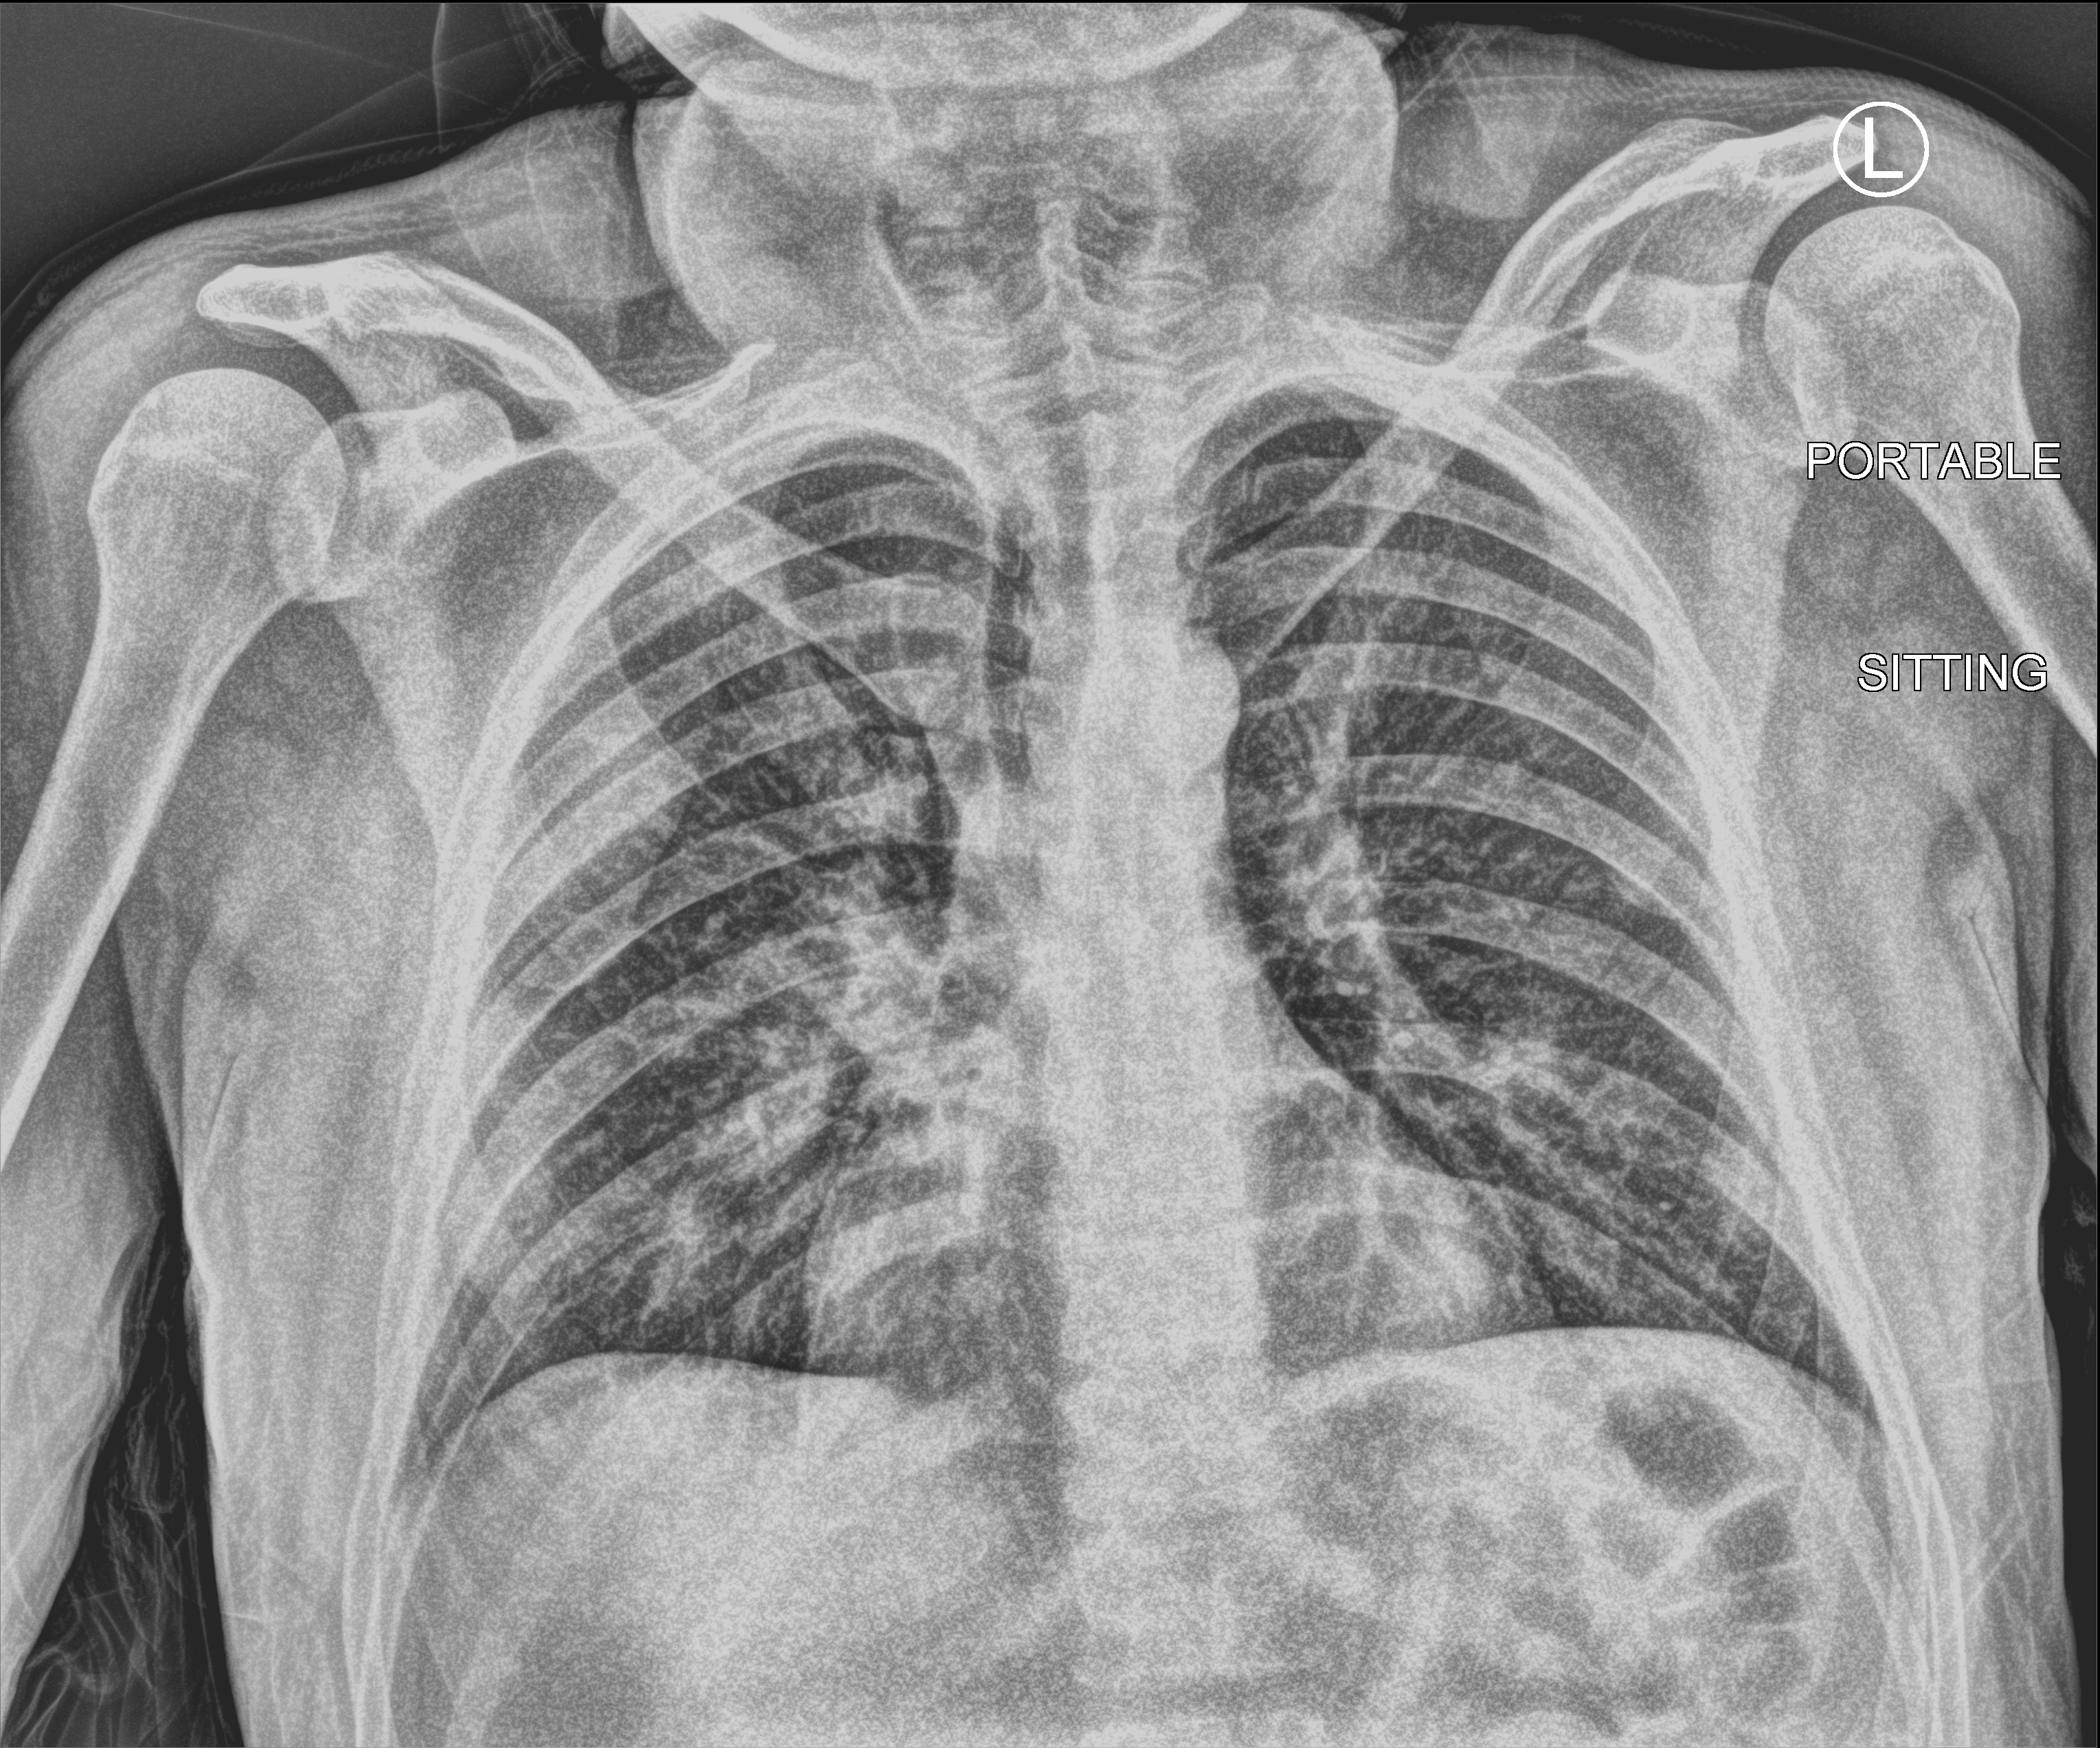
Portable chest radiograph; anteroposterior (AP) projection. Male patient hospitalised with COVID-19, age 18–59 years.
From the hospital-stay record, not from the radiograph (when in the stay this image was taken is not recorded): mechanically ventilated during this hospital stay: no.